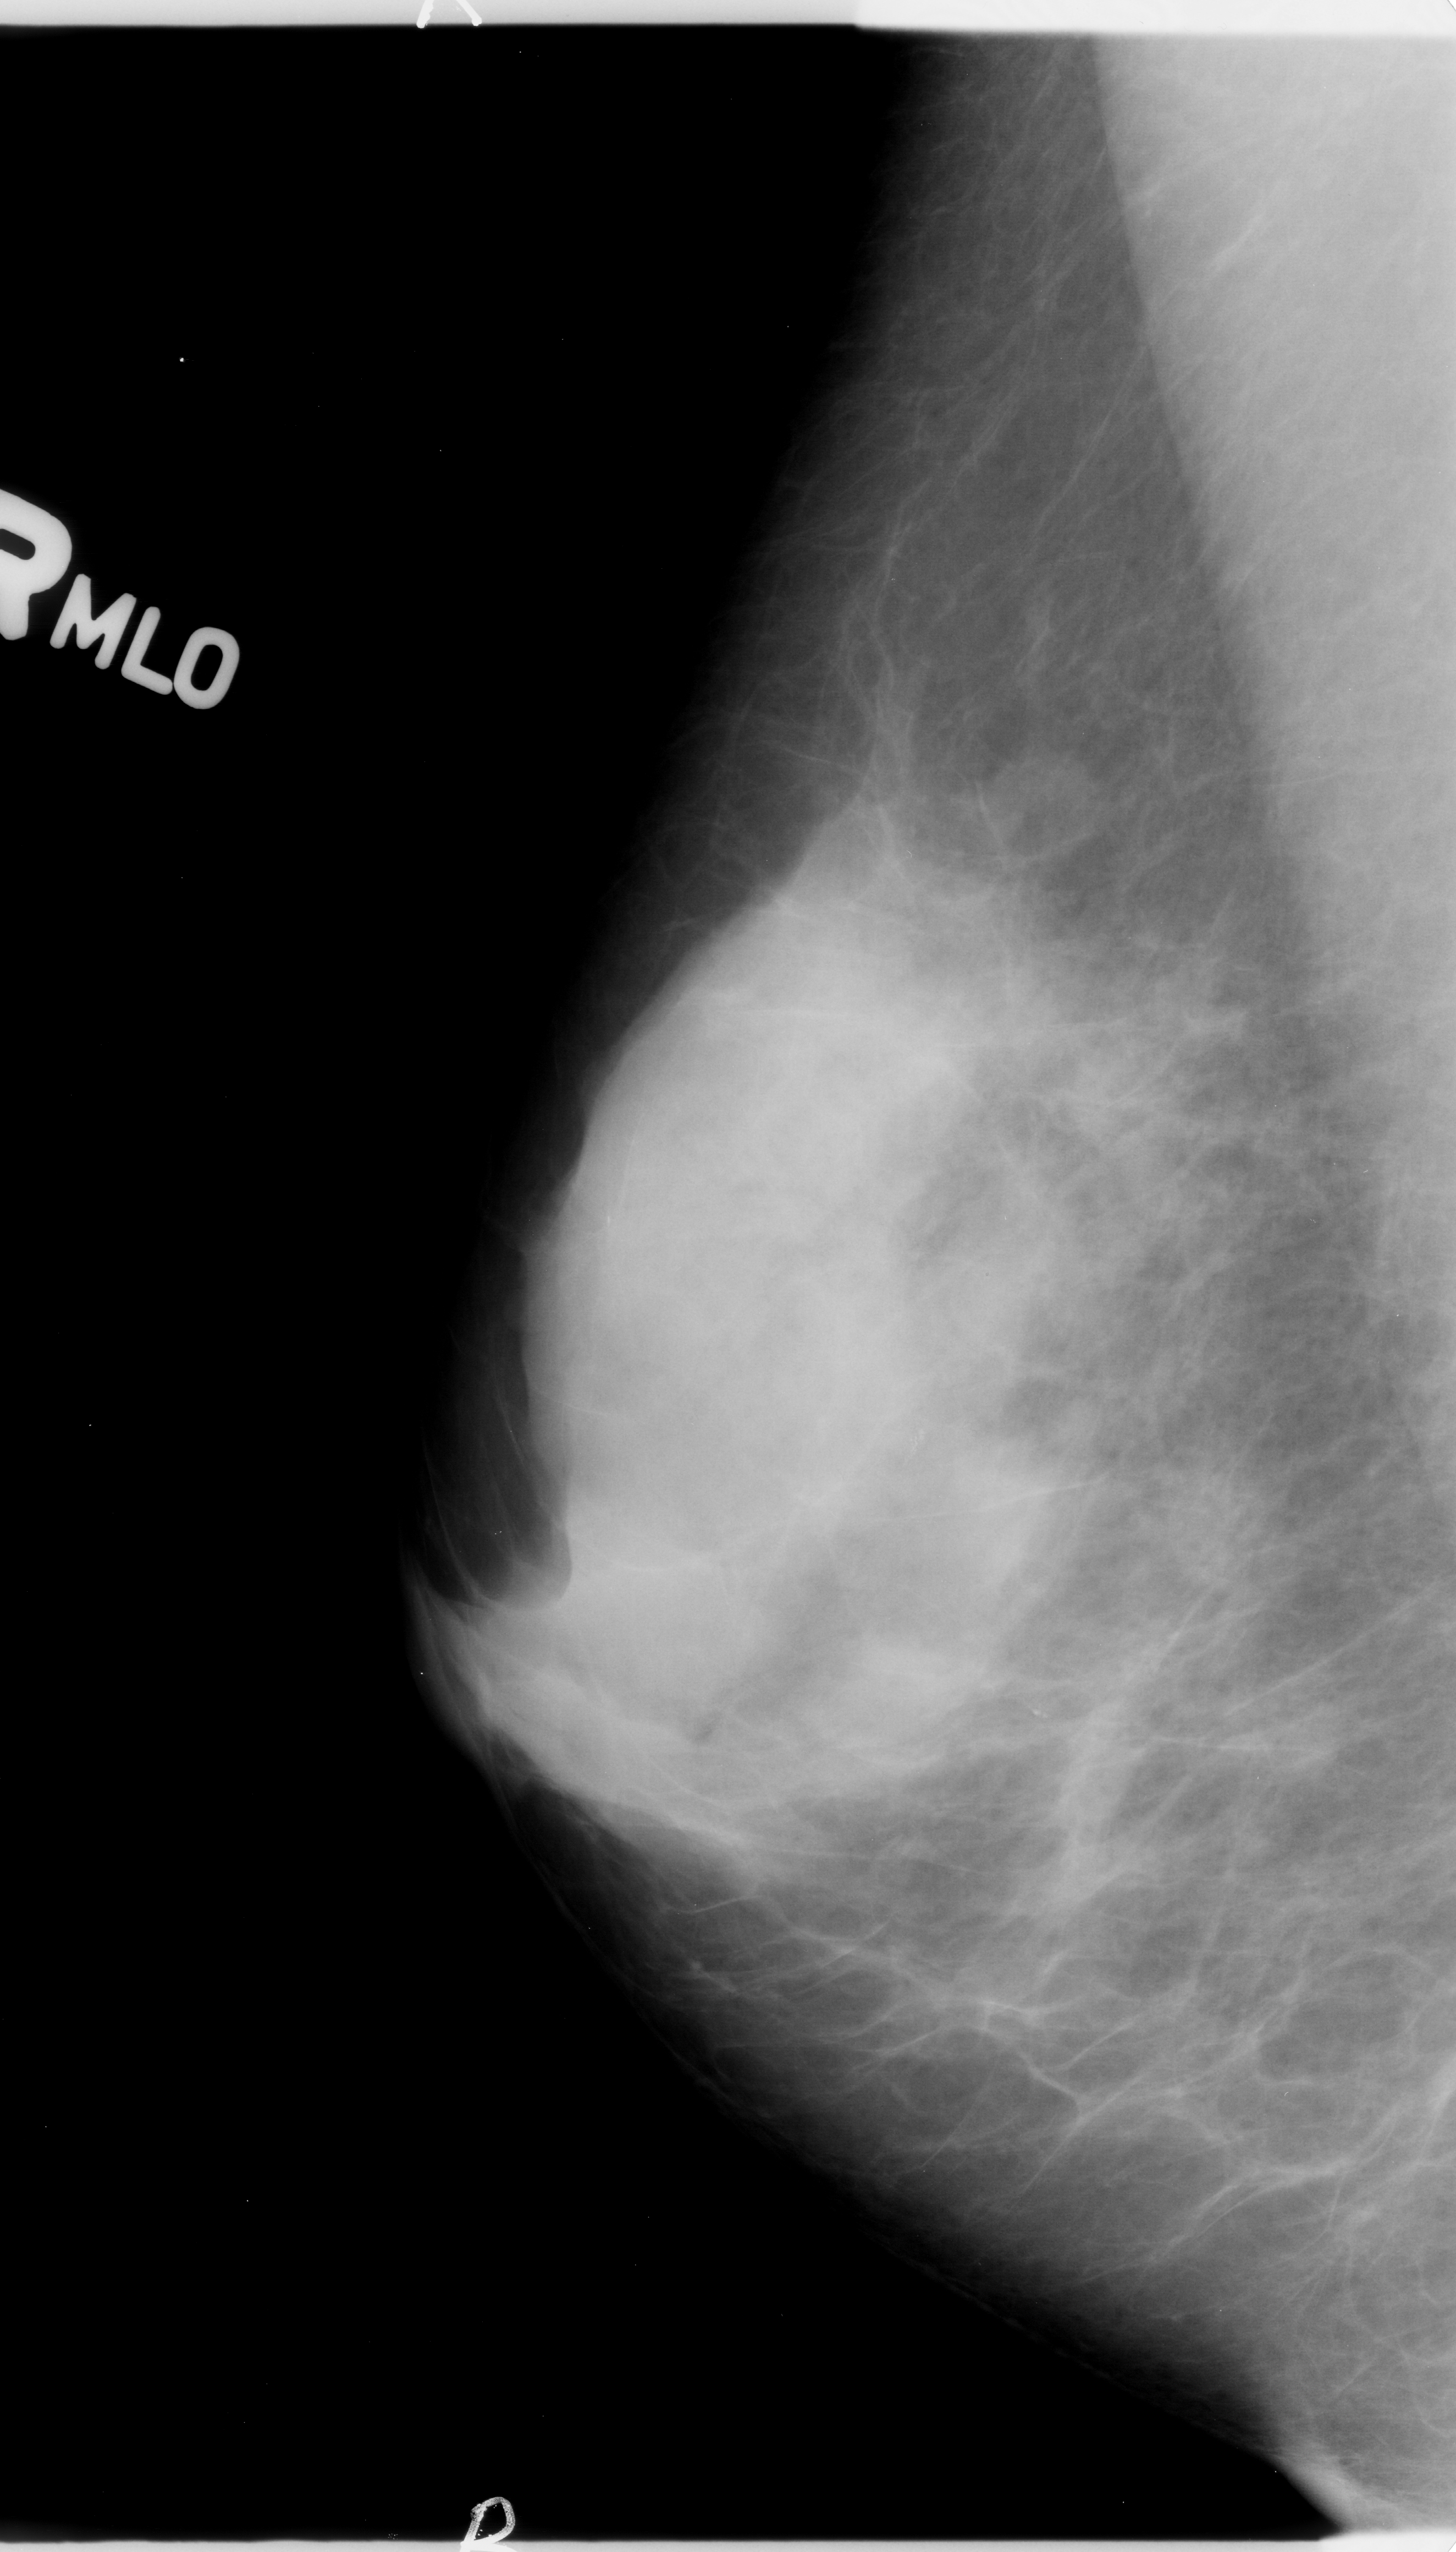
Mammogram (digitized film); right breast; mediolateral oblique (MLO) view; breast composition: extremely dense (BI-RADS density category 4 of 4); 1456 × 2552 image matrix.
Expert-marked regions of interest on this image (one box per marked abnormality):
- calcifications, morphology pleomorphic, distribution clustered; BI-RADS assessment category 4; subtlety rating 3 on a 1 (subtle) to 5 (obvious) scale; pathology (as recorded): benign: box from (x=857, y=1377) to (x=956, y=1554) px